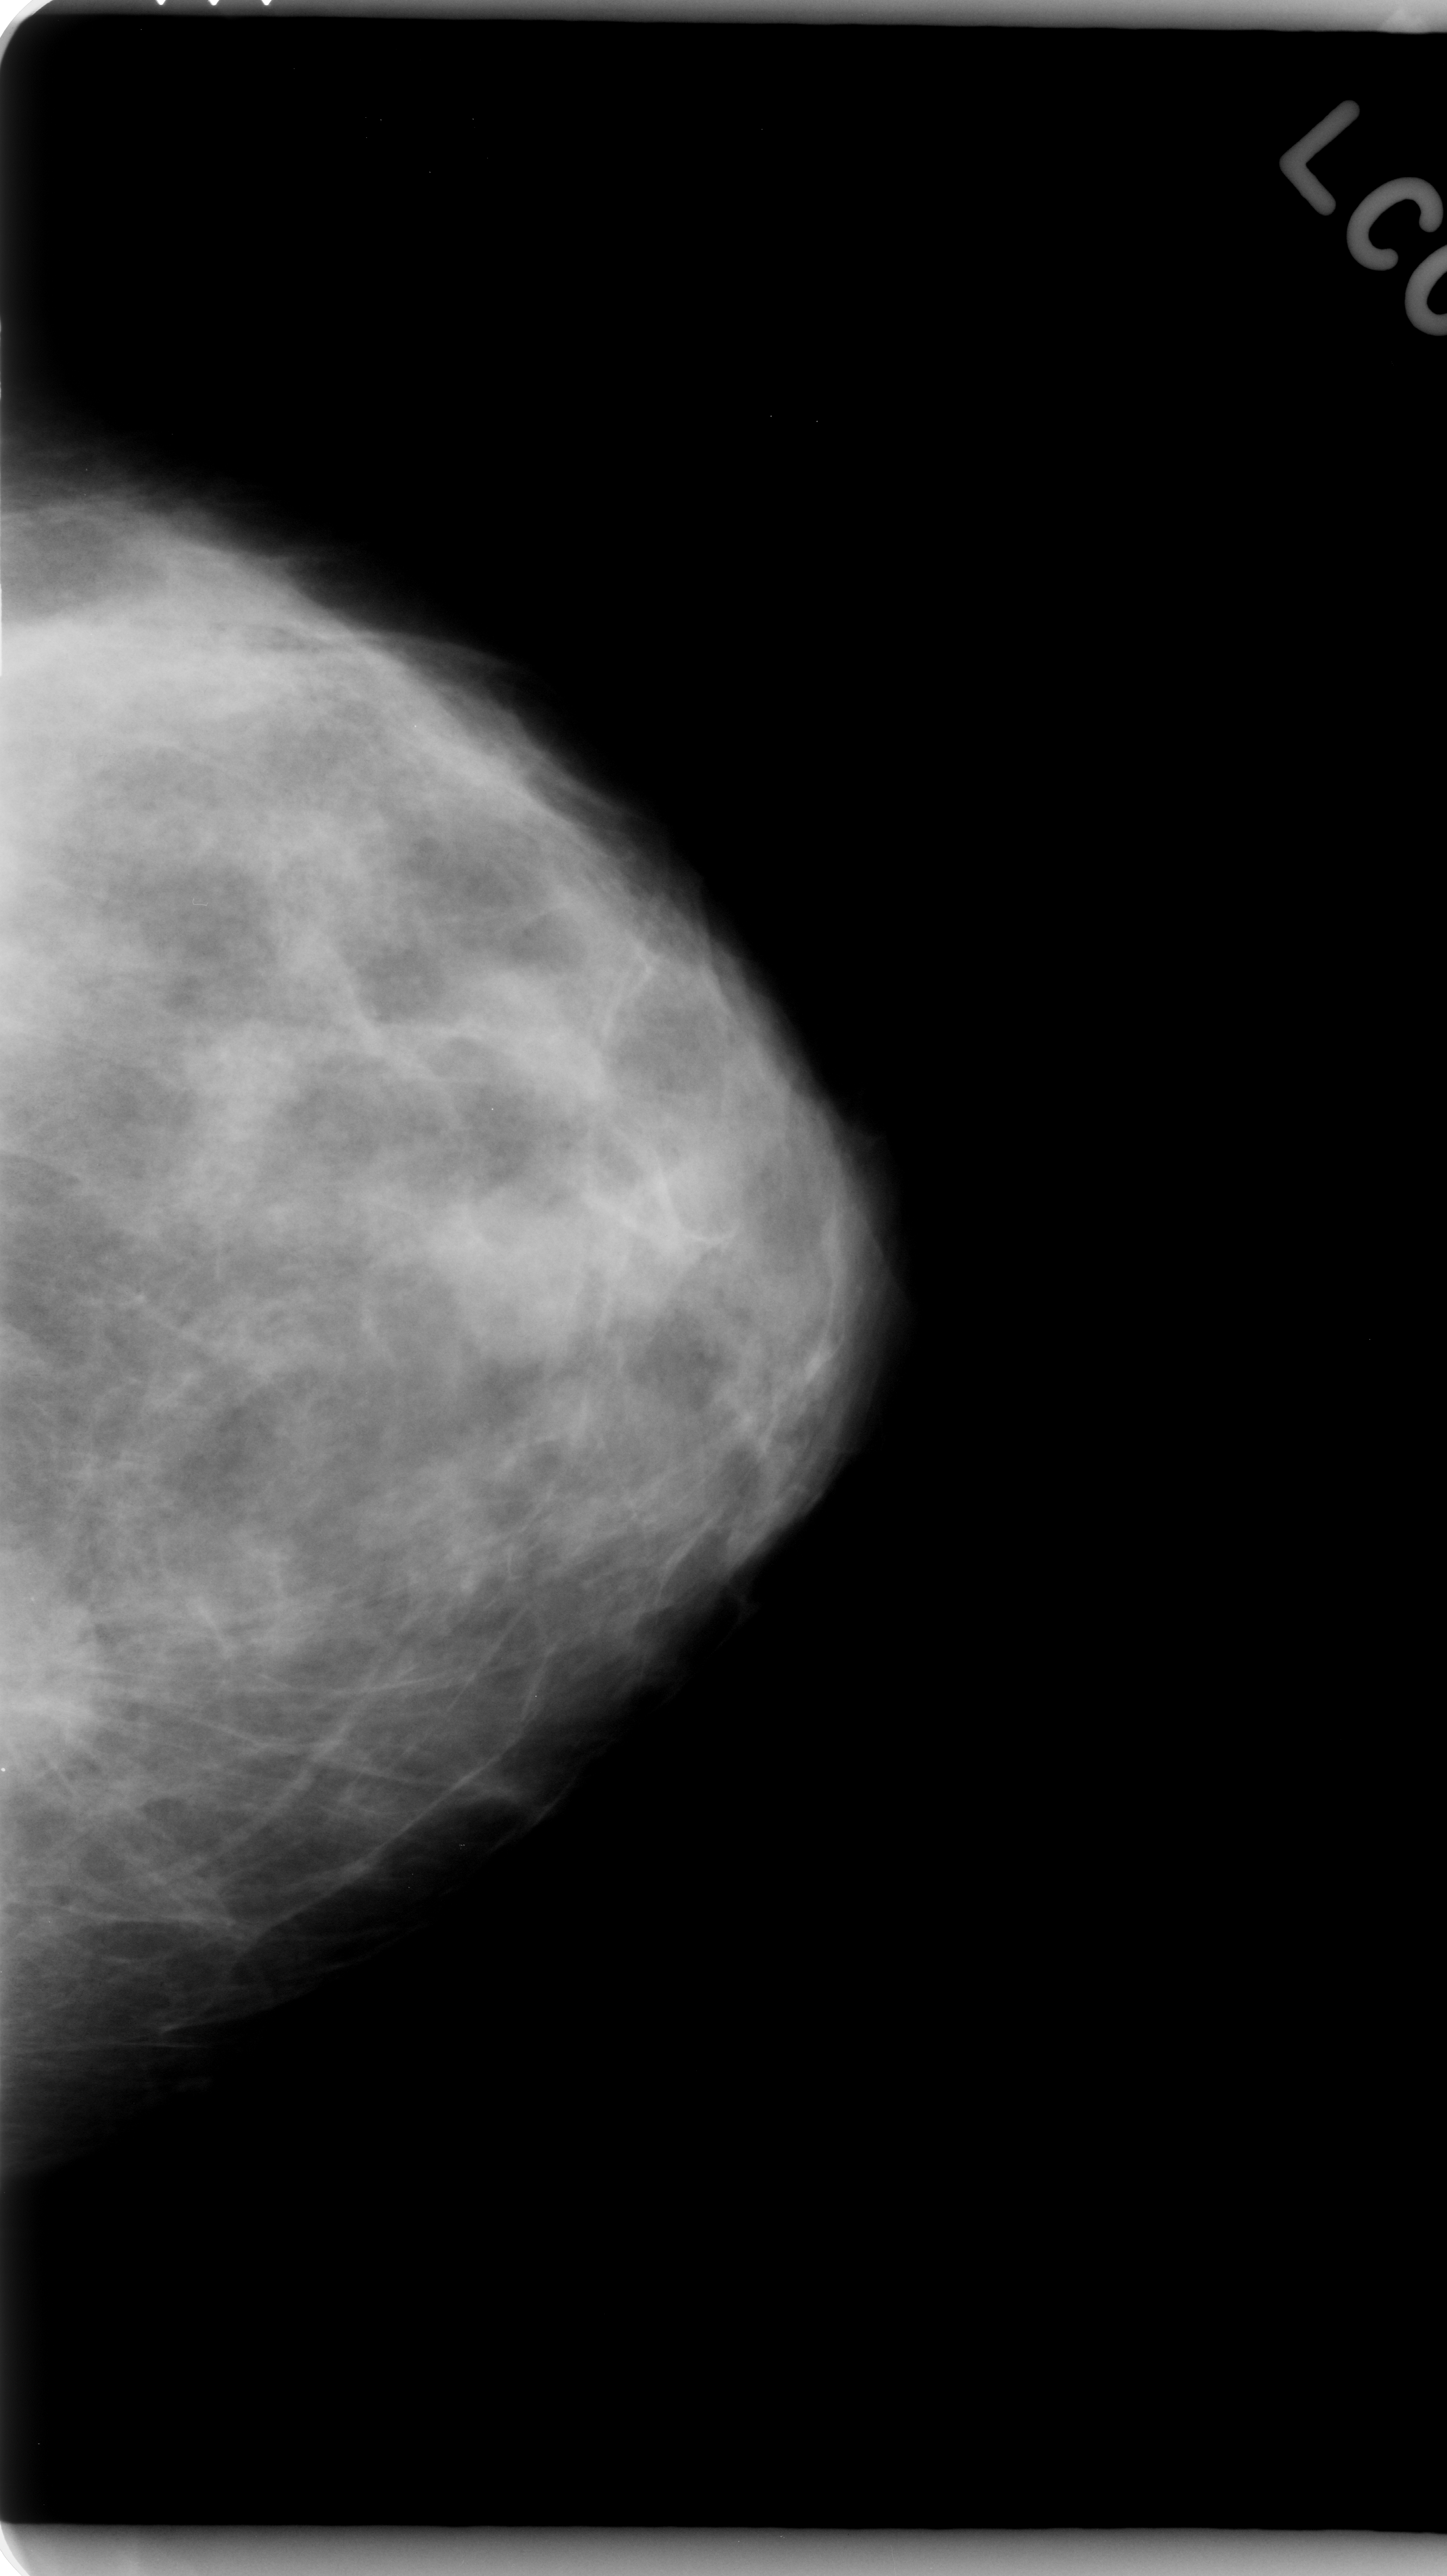
Scanned film-screen mammogram. Left breast. Craniocaudal (CC) view. BI-RADS breast density category 3 (scale 1–4). 1447 × 2576 image matrix.
Expert-marked regions of interest on this film, with their recorded descriptors:
- mass, shape irregular, margins spiculated; BI-RADS assessment category 5; pathology result (as recorded, not read from the image): malignant: bounding box <2,1570,157,1774> (left, top, right, bottom; pixels)